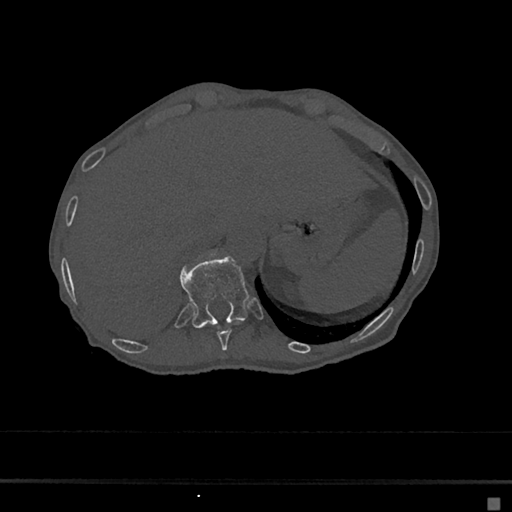
CT including the spine, one axial slice. Position 188 of 797 along the scan axis. 120 kVp. Bone window (W 1800 / L 400 HU). 512 × 512 image matrix, field of view 360 × 360 mm. Patient: female, 68 years. From the clinical record (not read from this slice): primary cancer: renal.
Annotated regions visible in this slice (semi-automatic segmentation, software-assisted and operator-edited):
- T10 vertebra: bounding box [x1, y1, x2, y2] px = [216, 321, 242, 351]
- T11 vertebra: [180, 256, 249, 328]